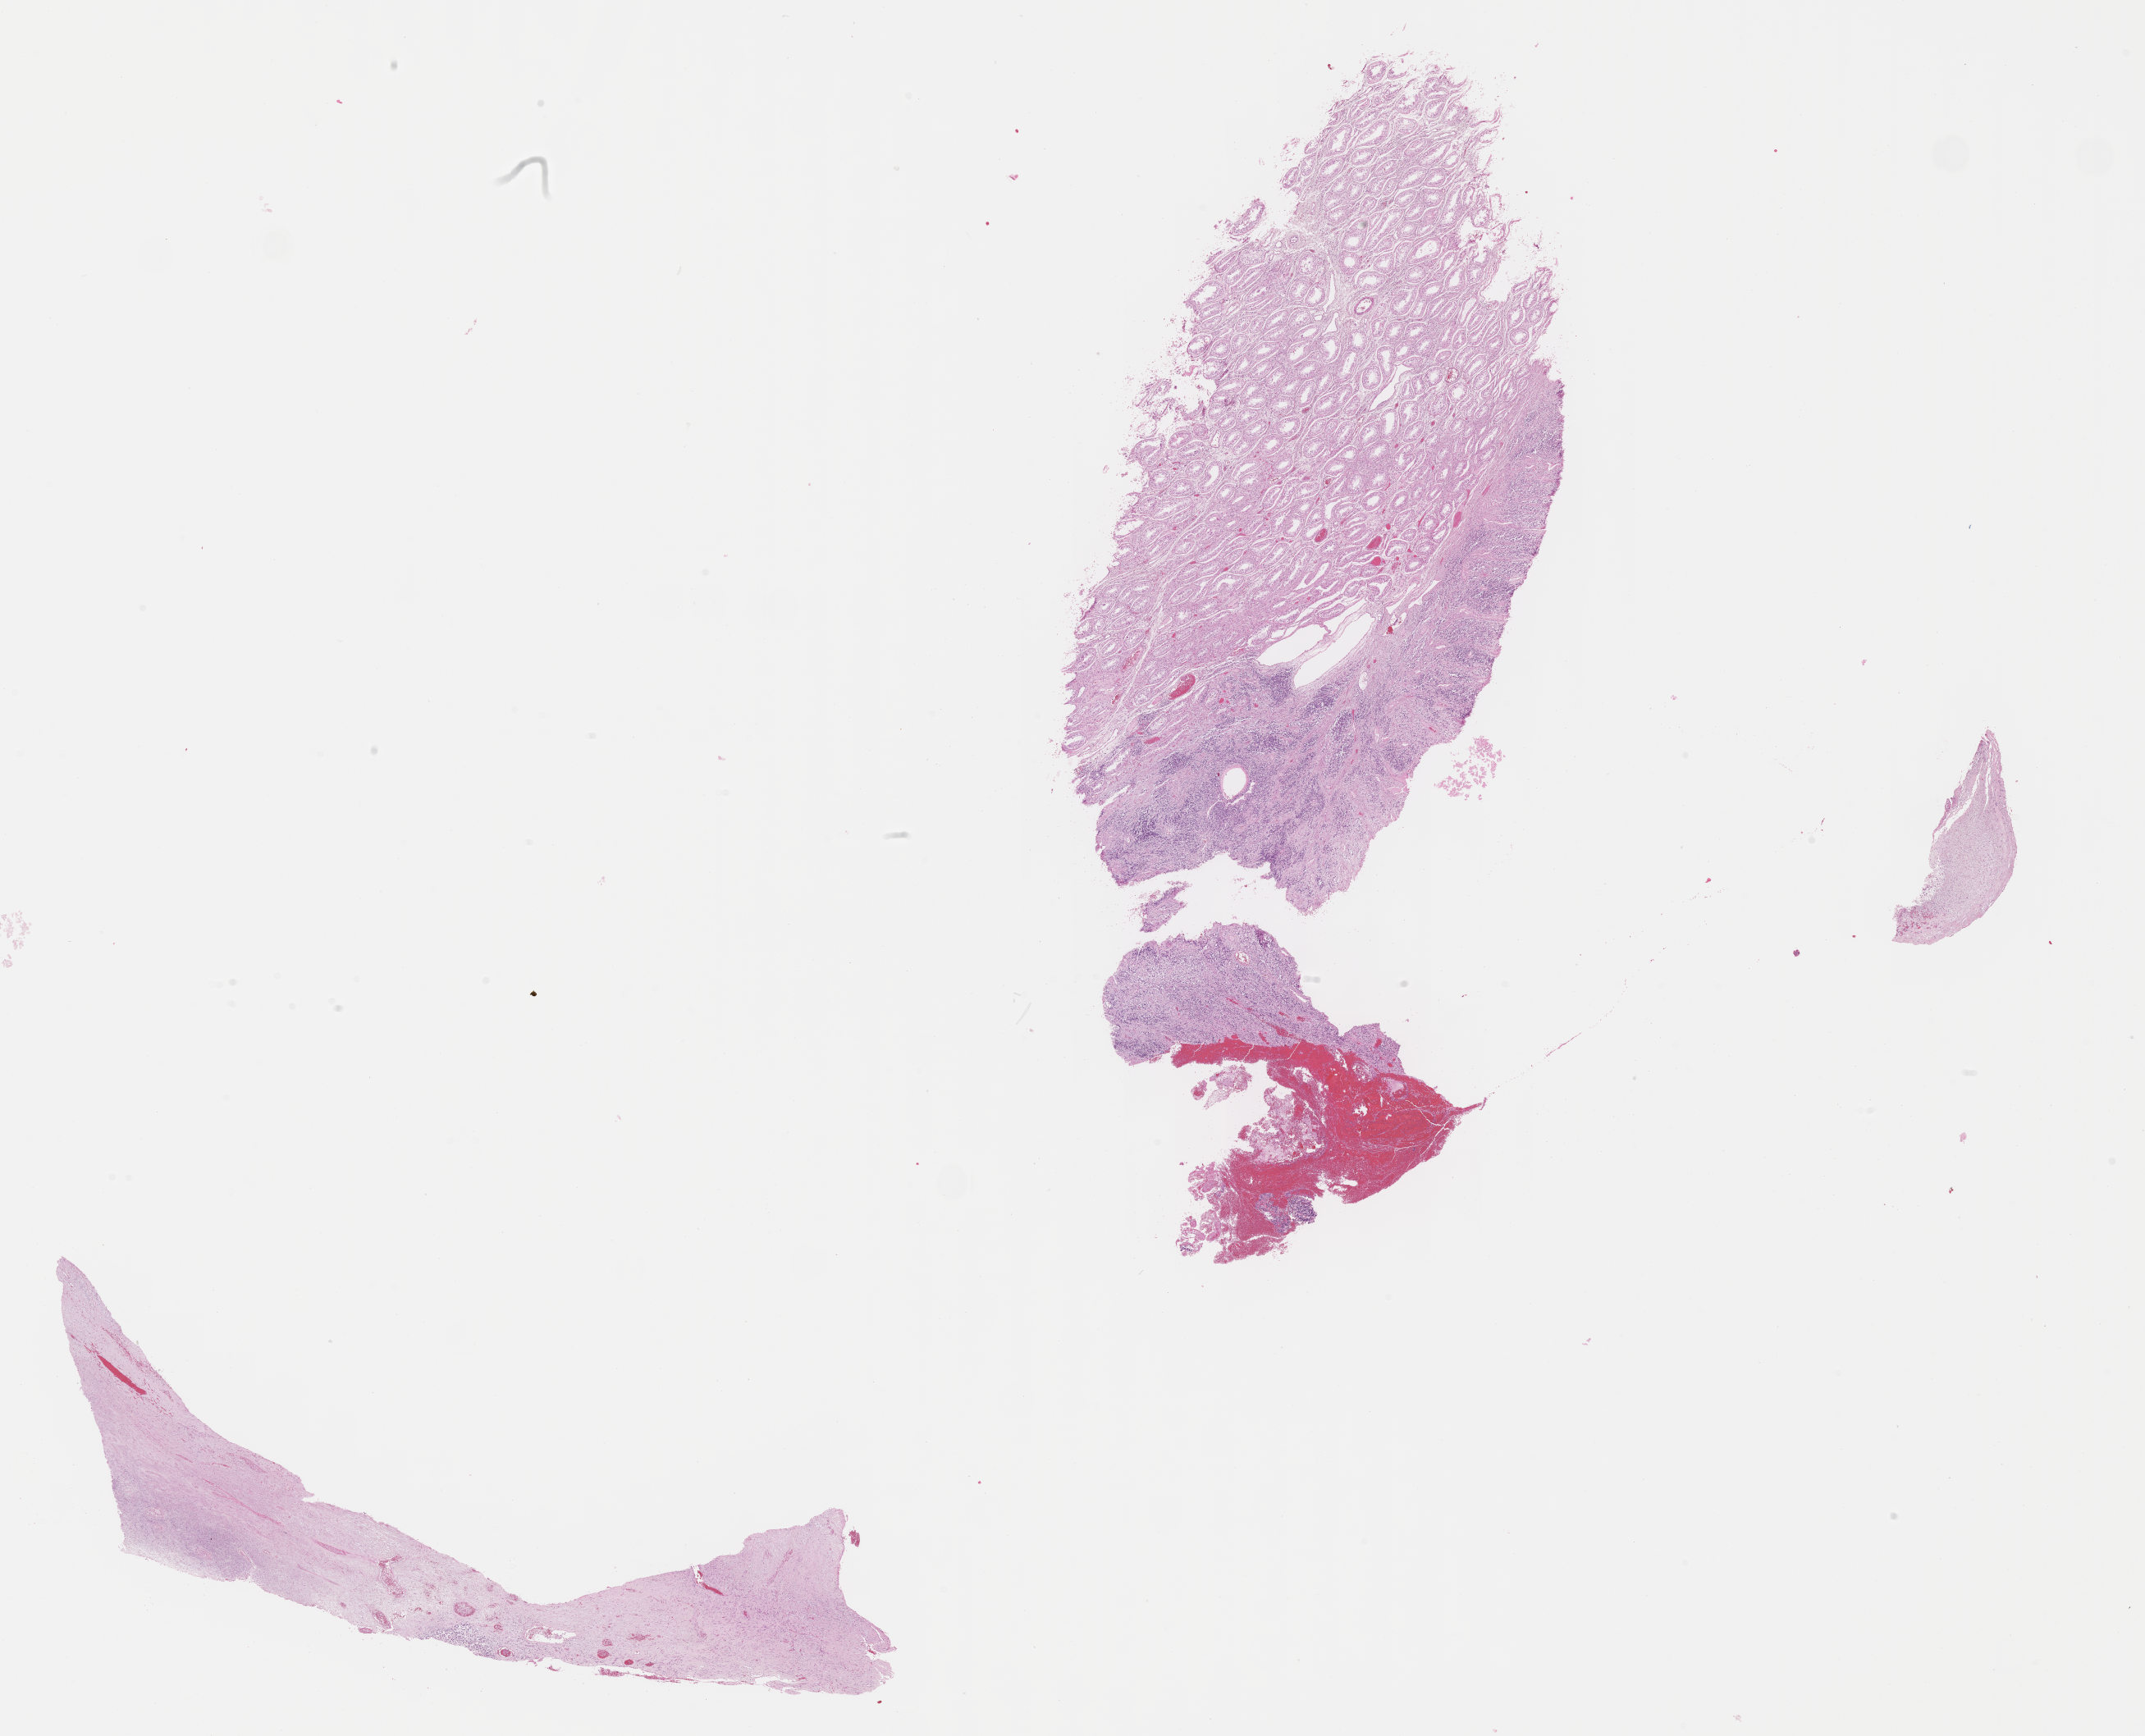
Hematoxylin and eosin (H&E) whole-slide image of tumor tissue, a low-resolution overview of the entire scanned area, about 21.1 x 17.1 mm, formalin-fixed, paraffin-embedded (FFPE) tissue, site: paratestes. Patient: male, age 20.2 years at diagnosis.
Metastatic status at presentation (as recorded): non-metastatic (unconfirmed). Diagnosis: rhabdomyosarcoma; histological classification: embryonal rhabdomyosarcoma.